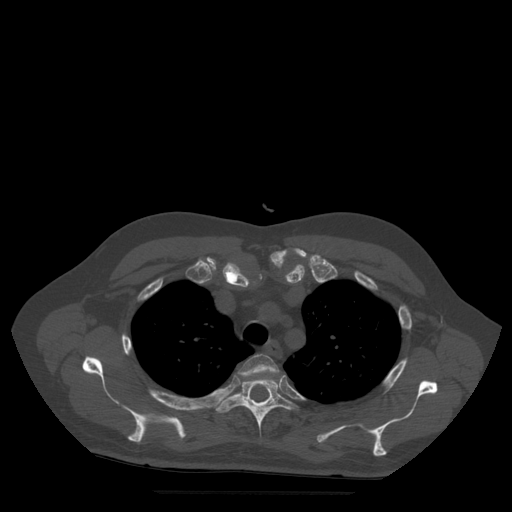
CT including the spine, one axial slice; position 396 of 522 along the scan axis; bone window (W 1800 / L 400 HU); 1.25 mm slice thickness; 512 × 512 image matrix, field of view 420 × 420 mm. Patient age 72 years. From the clinical record (not read from this slice): primary cancer: prostate.
Structures marked on this image (semi-automatically segmented with operator editing):
- T3 vertebra: bounding box (x1, y1, x2, y2) in pixels: (238, 355, 280, 382)
- T4 vertebra: (216, 377, 298, 437)